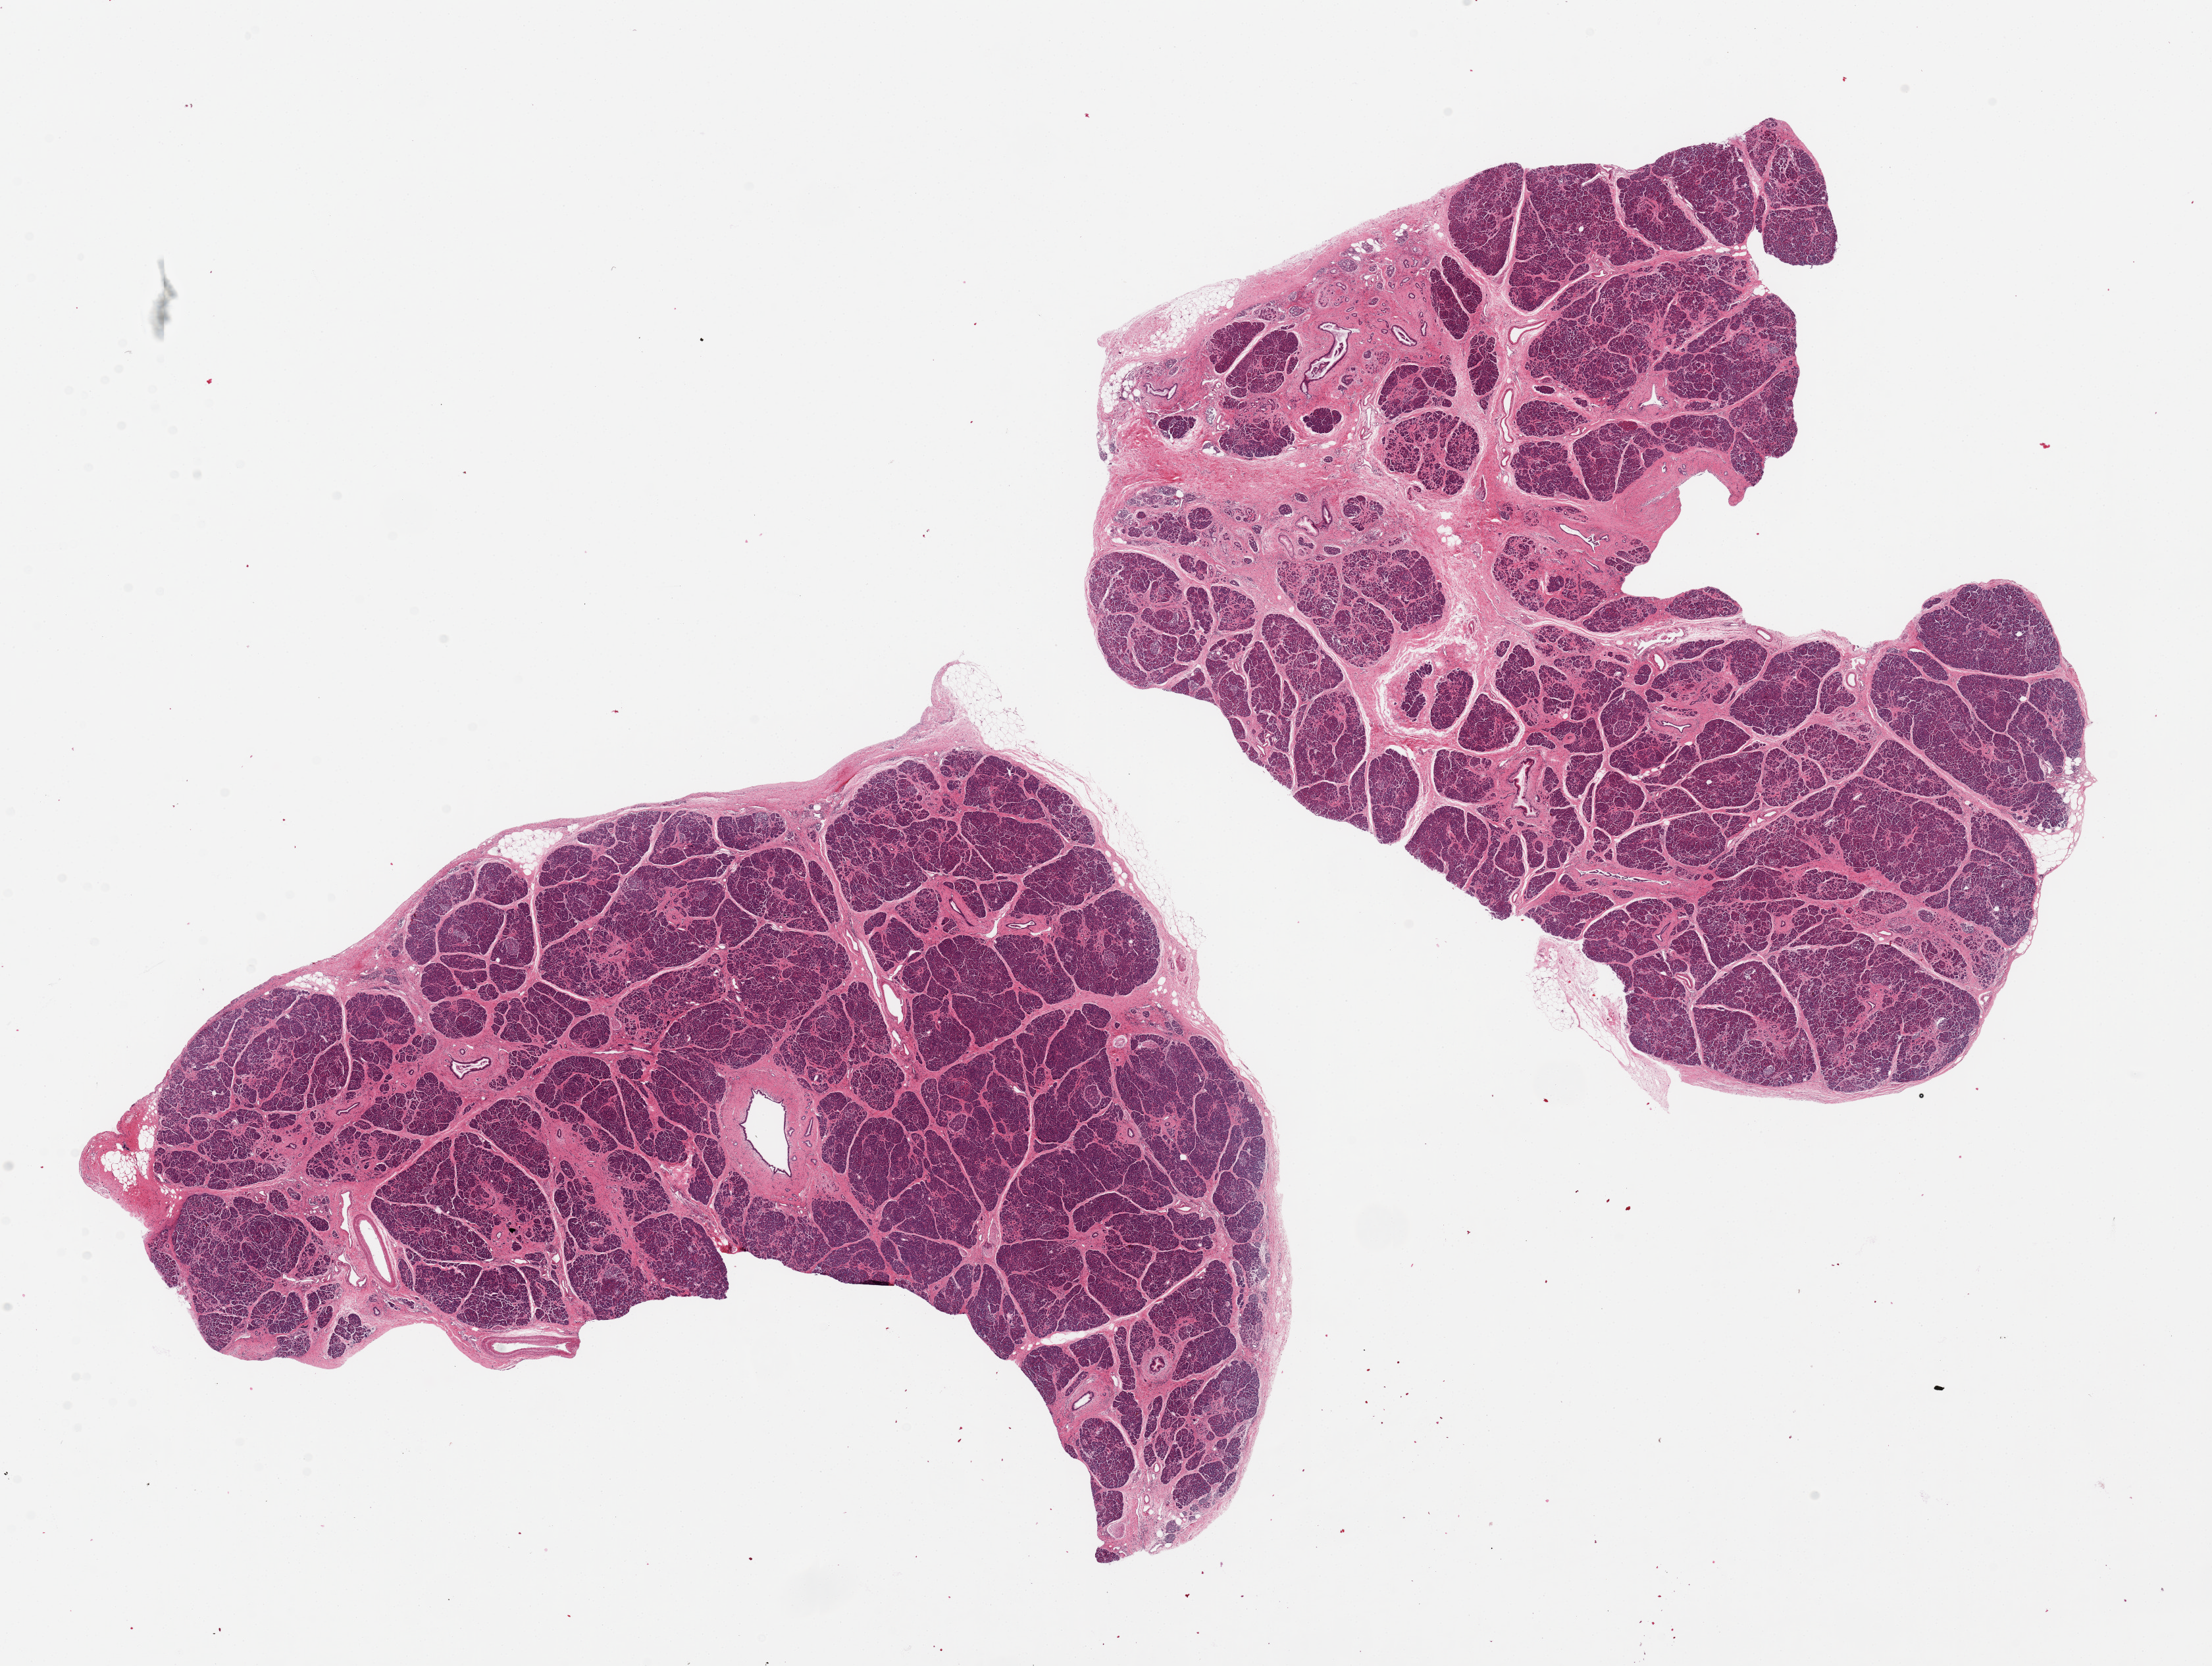
H&E whole-slide image, brightfield — a low-resolution overview of the entire scanned area, about 26.6 x 20.0 mm (from a 20x scan), PAXgene-fixed paraffin-embedded (PFPE) section, section of pancreas (target tissue), donor tissue sample. Female donor.
- reviewer comment on this tissue sample: 2 pieces, 13x11 & 13.5x11mm; interstitial fibrosis s/o remote pancreatitis, Islets well- visualized